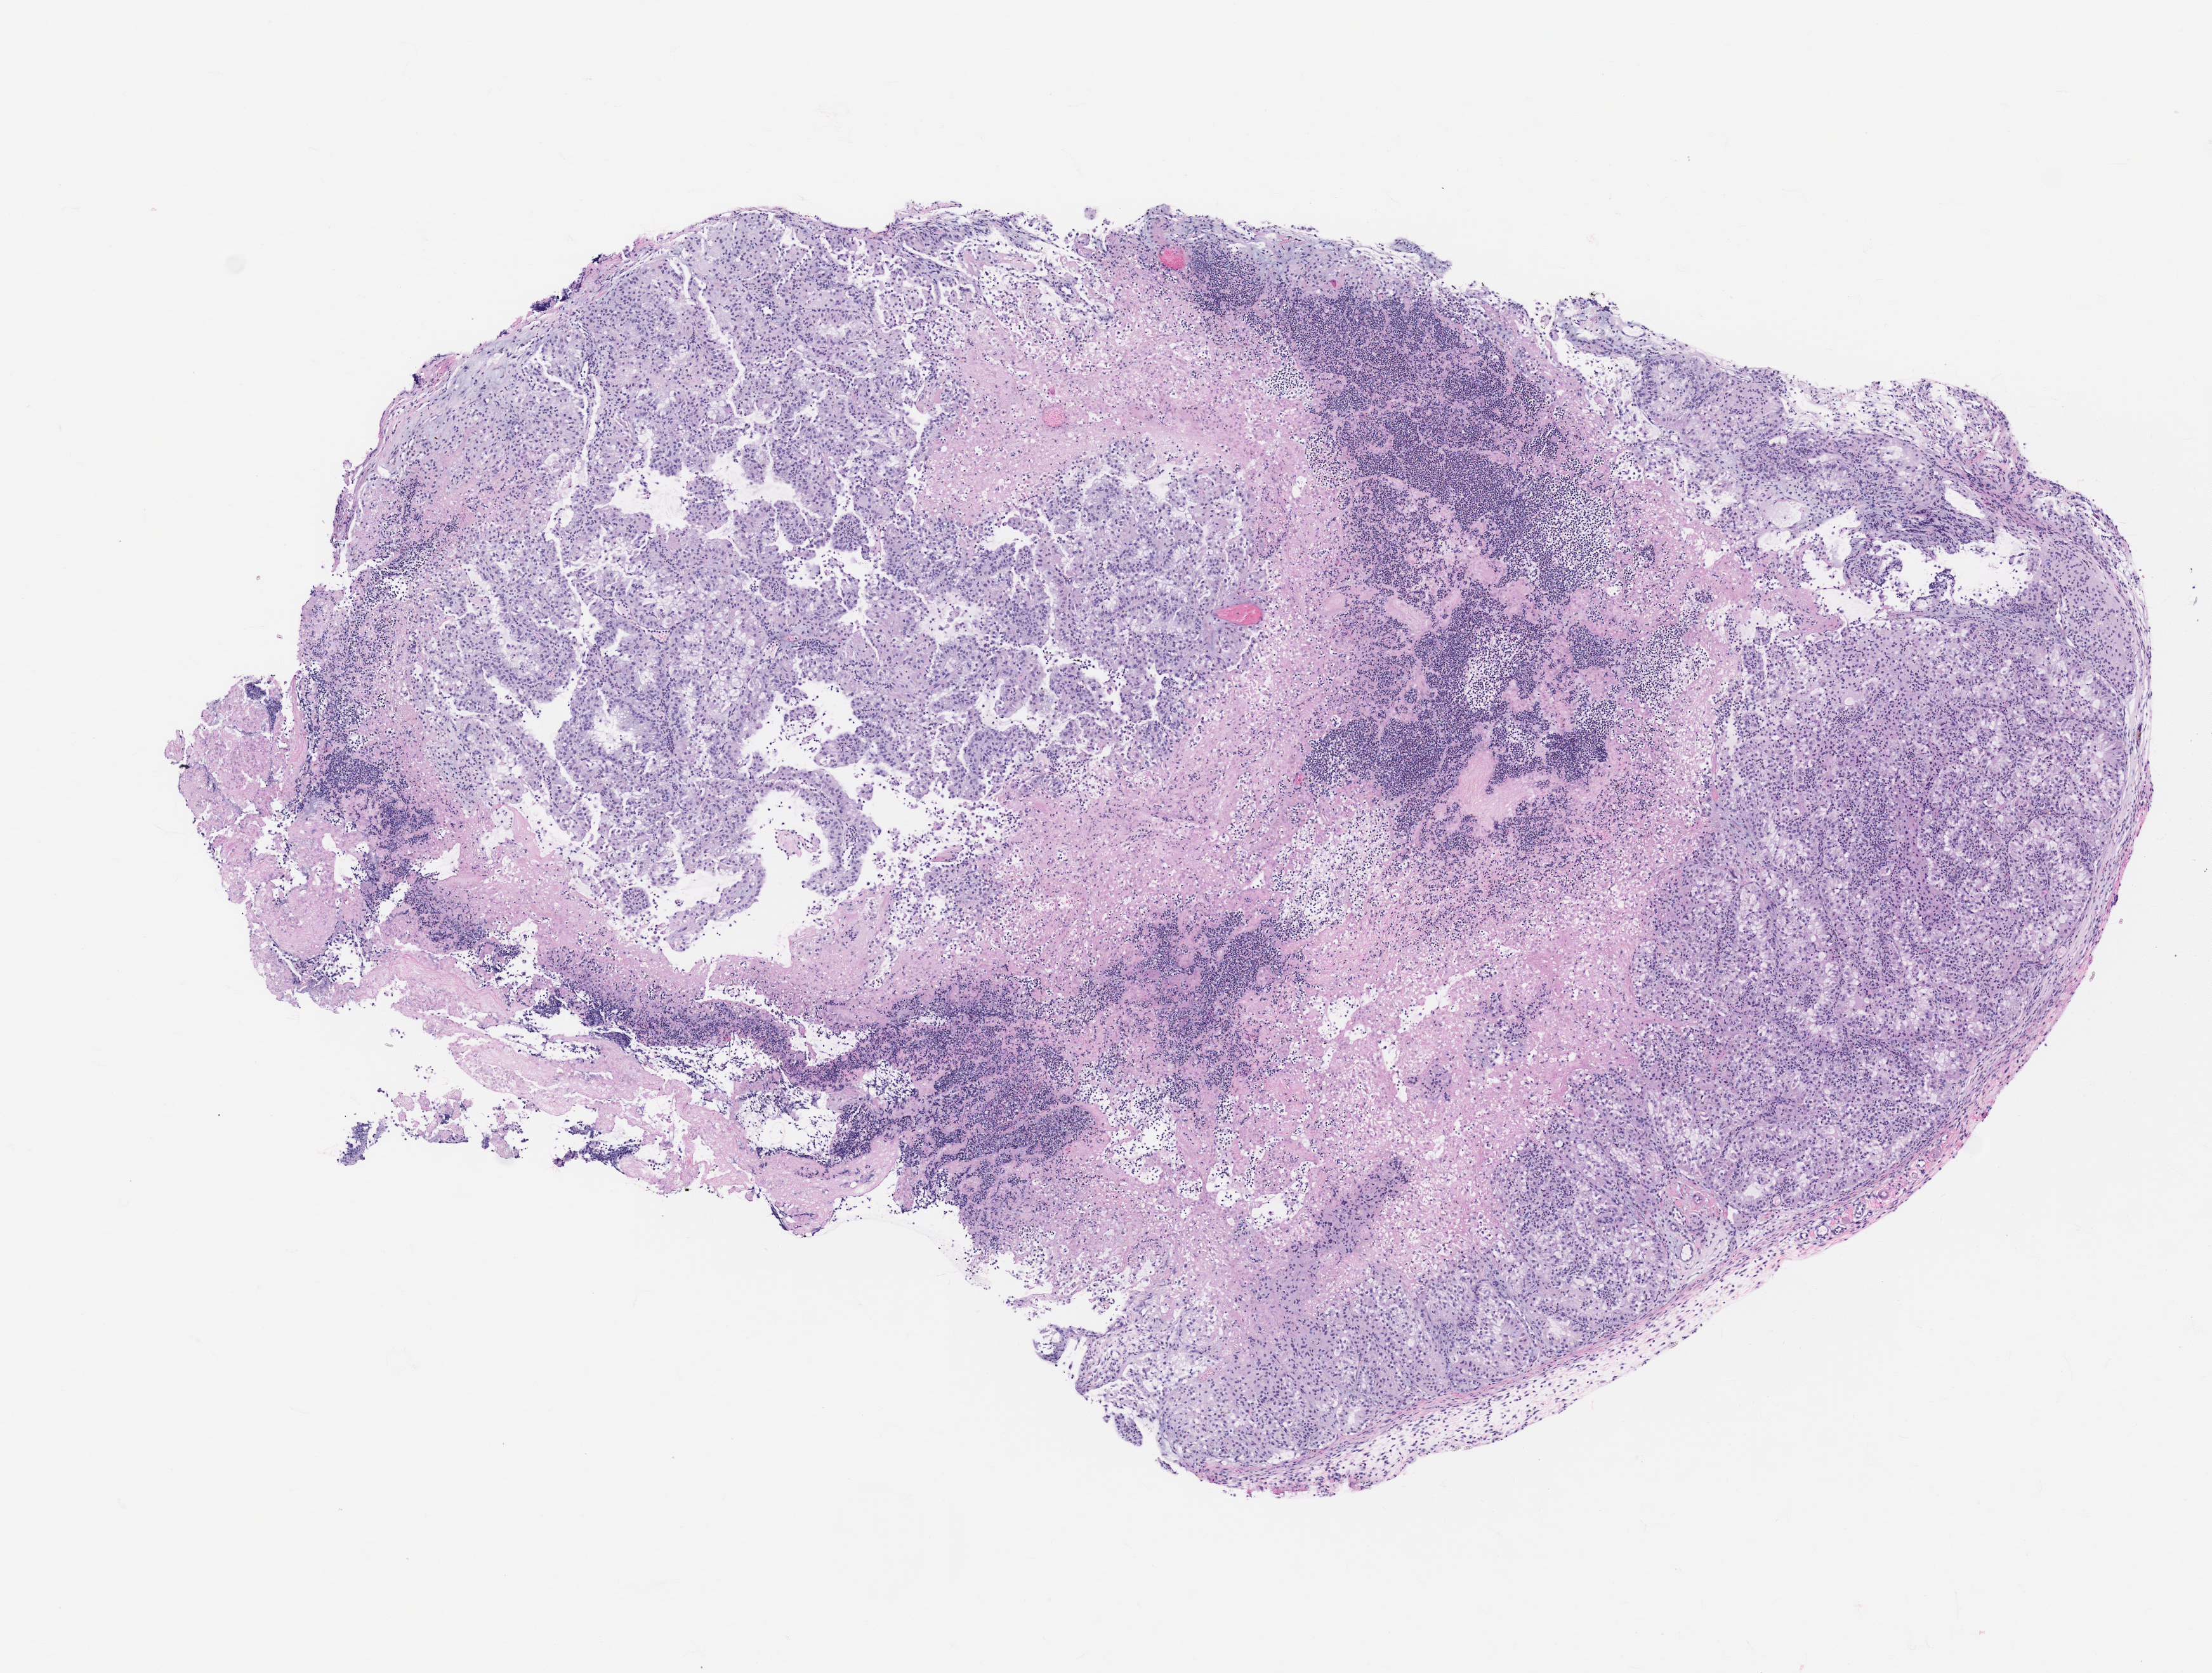
Whole-slide image, H&E: patient-derived xenograft (human tumor grown in a mouse), passage 0, low-resolution overview of the scanned area, about 7.0 x 5.3 mm, FFPE section, tumor site category: genitourinary tract.
Originating patient diagnosis: Renal Cell Carcinoma, Not Otherwise Specified.